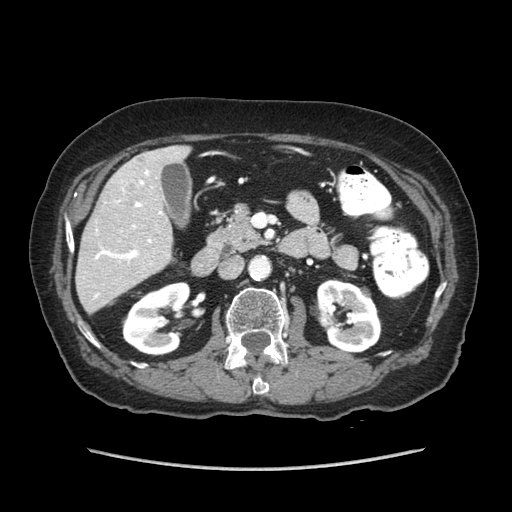
Contrast-enhanced abdominal CT (liver protocol), one axial slice; position 28 of 89 along the scan axis; 140 kVp; soft-tissue window (W 400 / L 40 HU); 512 × 512 image matrix, field of view 360 × 360 mm. Case-level facts recorded for this patient, not image findings: diagnosis: hepatocellular carcinoma (patient treated with transarterial chemoembolisation; whether this scan precedes or follows treatment is not stated here); TNM stage (as recorded): Stage-IIIA; Child-Pugh class: A; tumour size: 11 cm.
Outlined on this slice (semi-automatically segmented with operator editing):
- liver parenchyma outside the tumour (the mass and vessels are separate outlines, so this box may not span the whole liver): bounding box <76,146,190,312> (left, top, right, bottom; pixels)
- mass: <103,153,160,201>
- liver vessels: <94,170,162,298>